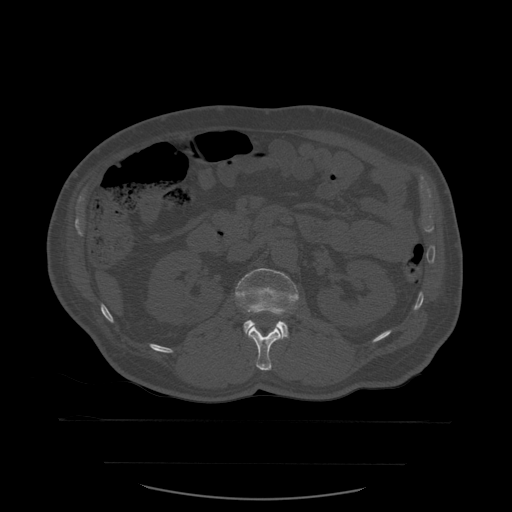
CT including the spine, one axial slice; position 233 of 590 along the scan axis; bone window (W 1800 / L 400 HU); 512 × 512 image matrix, field of view 479 × 479 mm. Patient age 71 years. From the clinical record (not read from this slice): primary cancer: lung; vertebrae with lytic lesions (as recorded): T1, T2, L5, S1.
Annotated regions visible in this slice (semi-automatic segmentation, software-assisted and operator-edited):
- L1 vertebra: bounding box <248,326,282,371> (left, top, right, bottom; pixels)
- L2 vertebra: <235,269,299,340>